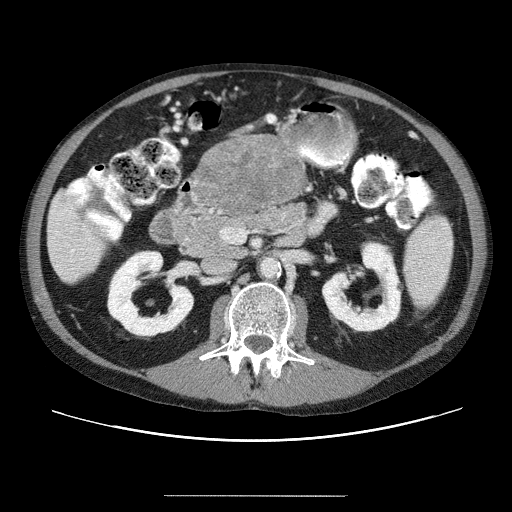
Contrast-enhanced abdominal CT (liver protocol), one axial slice. Slice 6 of 69 in the series (ordered by position). Soft-tissue window (W 400 / L 40 HU). 2.5 mm slice thickness. 512 × 512 image matrix, field of view 380 × 380 mm. From the clinical record (not read from this slice): diagnosis: hepatocellular carcinoma (patient treated with transarterial chemoembolisation; whether this scan precedes or follows treatment is not stated here); TNM stage (as recorded): Stage-IVB; Child-Pugh class: B; tumour differentiation: poorly differentiated; tumour nodularity: multinodular.
Annotated regions visible in this slice (semi-automatic segmentation, software-assisted and operator-edited):
- liver parenchyma outside the tumour (the mass and vessels are separate outlines, so this box may not span the whole liver): bounding box (x1, y1, x2, y2) in pixels: (48, 139, 300, 280)
- mass: (189, 140, 303, 219)
- liver vessels: (52, 243, 74, 258)